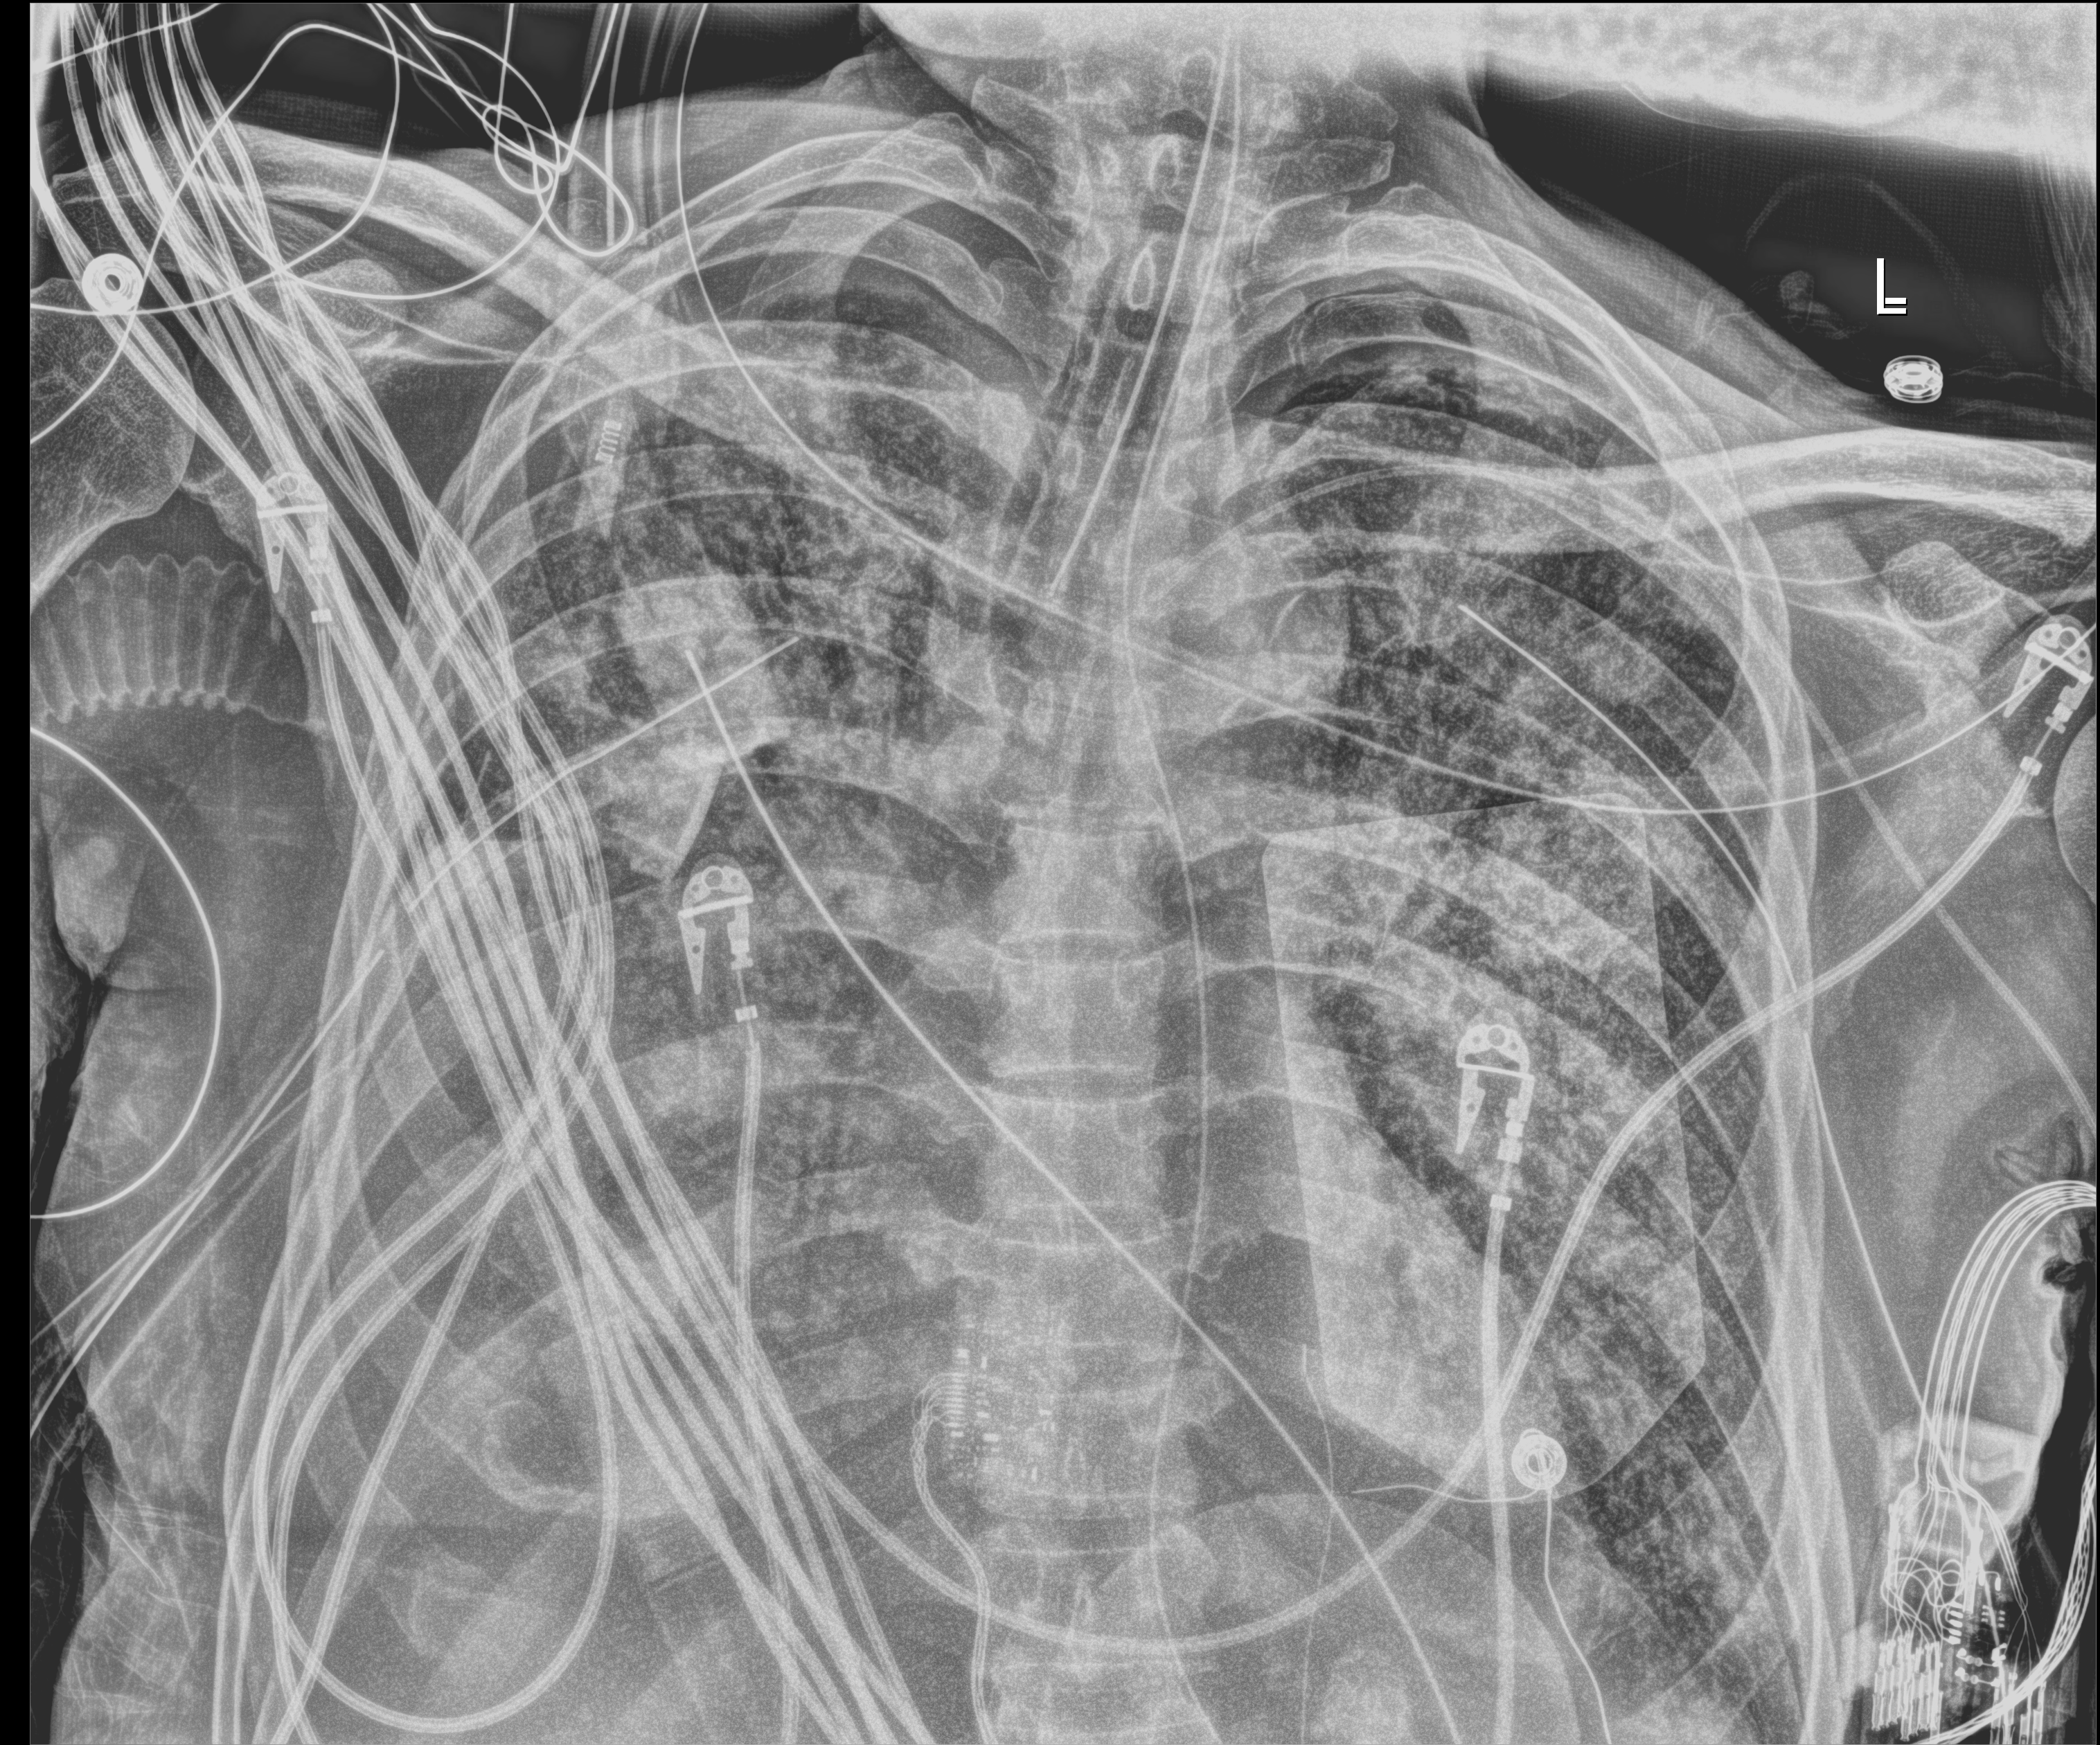
Chest X-ray (portable); anteroposterior (AP) projection. Male patient hospitalised with COVID-19, age 60–74 years.
Hospital-stay facts (about this admission, not read from this image; timing relative to this image not recorded): other chronic lung disease (admission record): no.